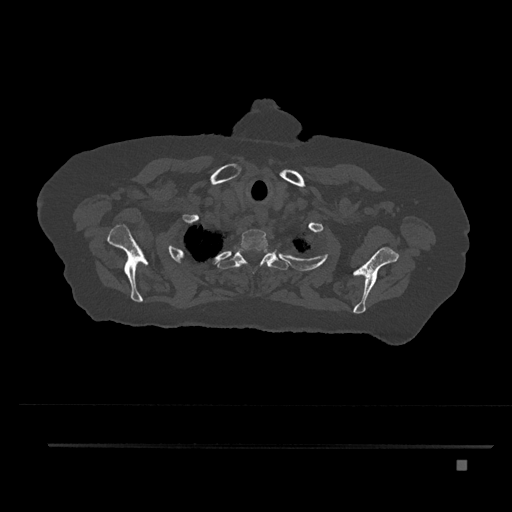
CT including the spine, one axial slice; position 680 of 797 along the scan axis; 120 kVp; bone window (W 1800 / L 400 HU); 0.5 mm slice thickness; 512 × 512 image matrix, field of view 437 × 437 mm. Female patient, age 76 years. From the clinical record (not read from this slice): primary cancer: lung; vertebrae with lytic lesions (as recorded): T11, L3.
Structures marked on this image (semi-automatically segmented with operator editing):
- T1 vertebra: bounding box [x1, y1, x2, y2] px = [241, 229, 273, 251]
- T2 vertebra: [217, 249, 288, 270]